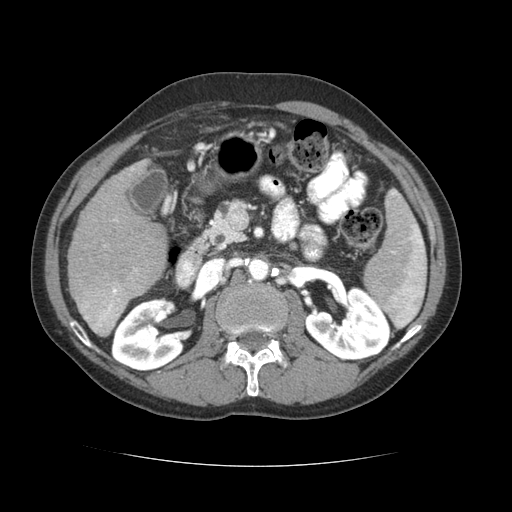
Contrast-enhanced abdominal CT (liver protocol), one axial slice; slice 29 of 69 in the series (ordered by position); reconstruction kernel STANDARD; soft-tissue window (W 400 / L 40 HU); 2.5 mm slice thickness; 512 × 512 image matrix, field of view 360 × 360 mm. Case-level facts recorded for this patient, not image findings: diagnosis: hepatocellular carcinoma (patient treated with transarterial chemoembolisation; whether this scan precedes or follows treatment is not stated here); TNM stage (as recorded): Stage-II; Child-Pugh class: B; tumour differentiation: poorly differentiated; tumour size: 2.6 cm.
Outlined on this slice (semi-automatic segmentation, software-assisted and operator-edited):
- liver parenchyma outside the tumour (the mass and vessels are separate outlines, so this box may not span the whole liver): box from (x=68, y=160) to (x=166, y=336) px
- liver vessels: (x=81, y=167)–(x=137, y=332)